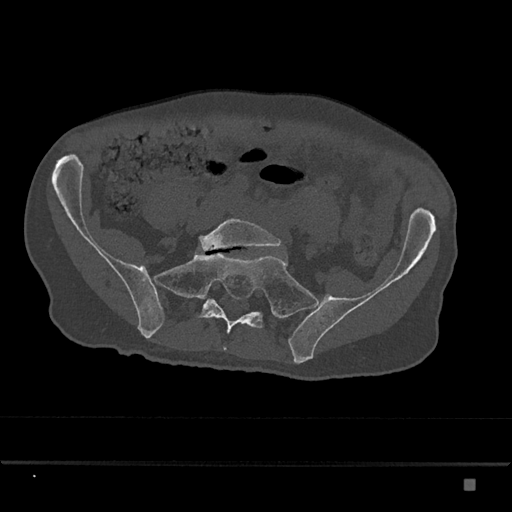
CT including the spine, one axial slice; bone window (W 1800 / L 400 HU); 0.5 mm slice thickness; 512 × 512 image matrix. Patient: male, 72 years. Case-level facts recorded for this patient, not image findings: primary cancer: prostate.
Annotated regions visible in this slice (semi-automatically segmented with operator editing):
- L5 vertebra: bounding box <199,218,281,251> (left, top, right, bottom; pixels)